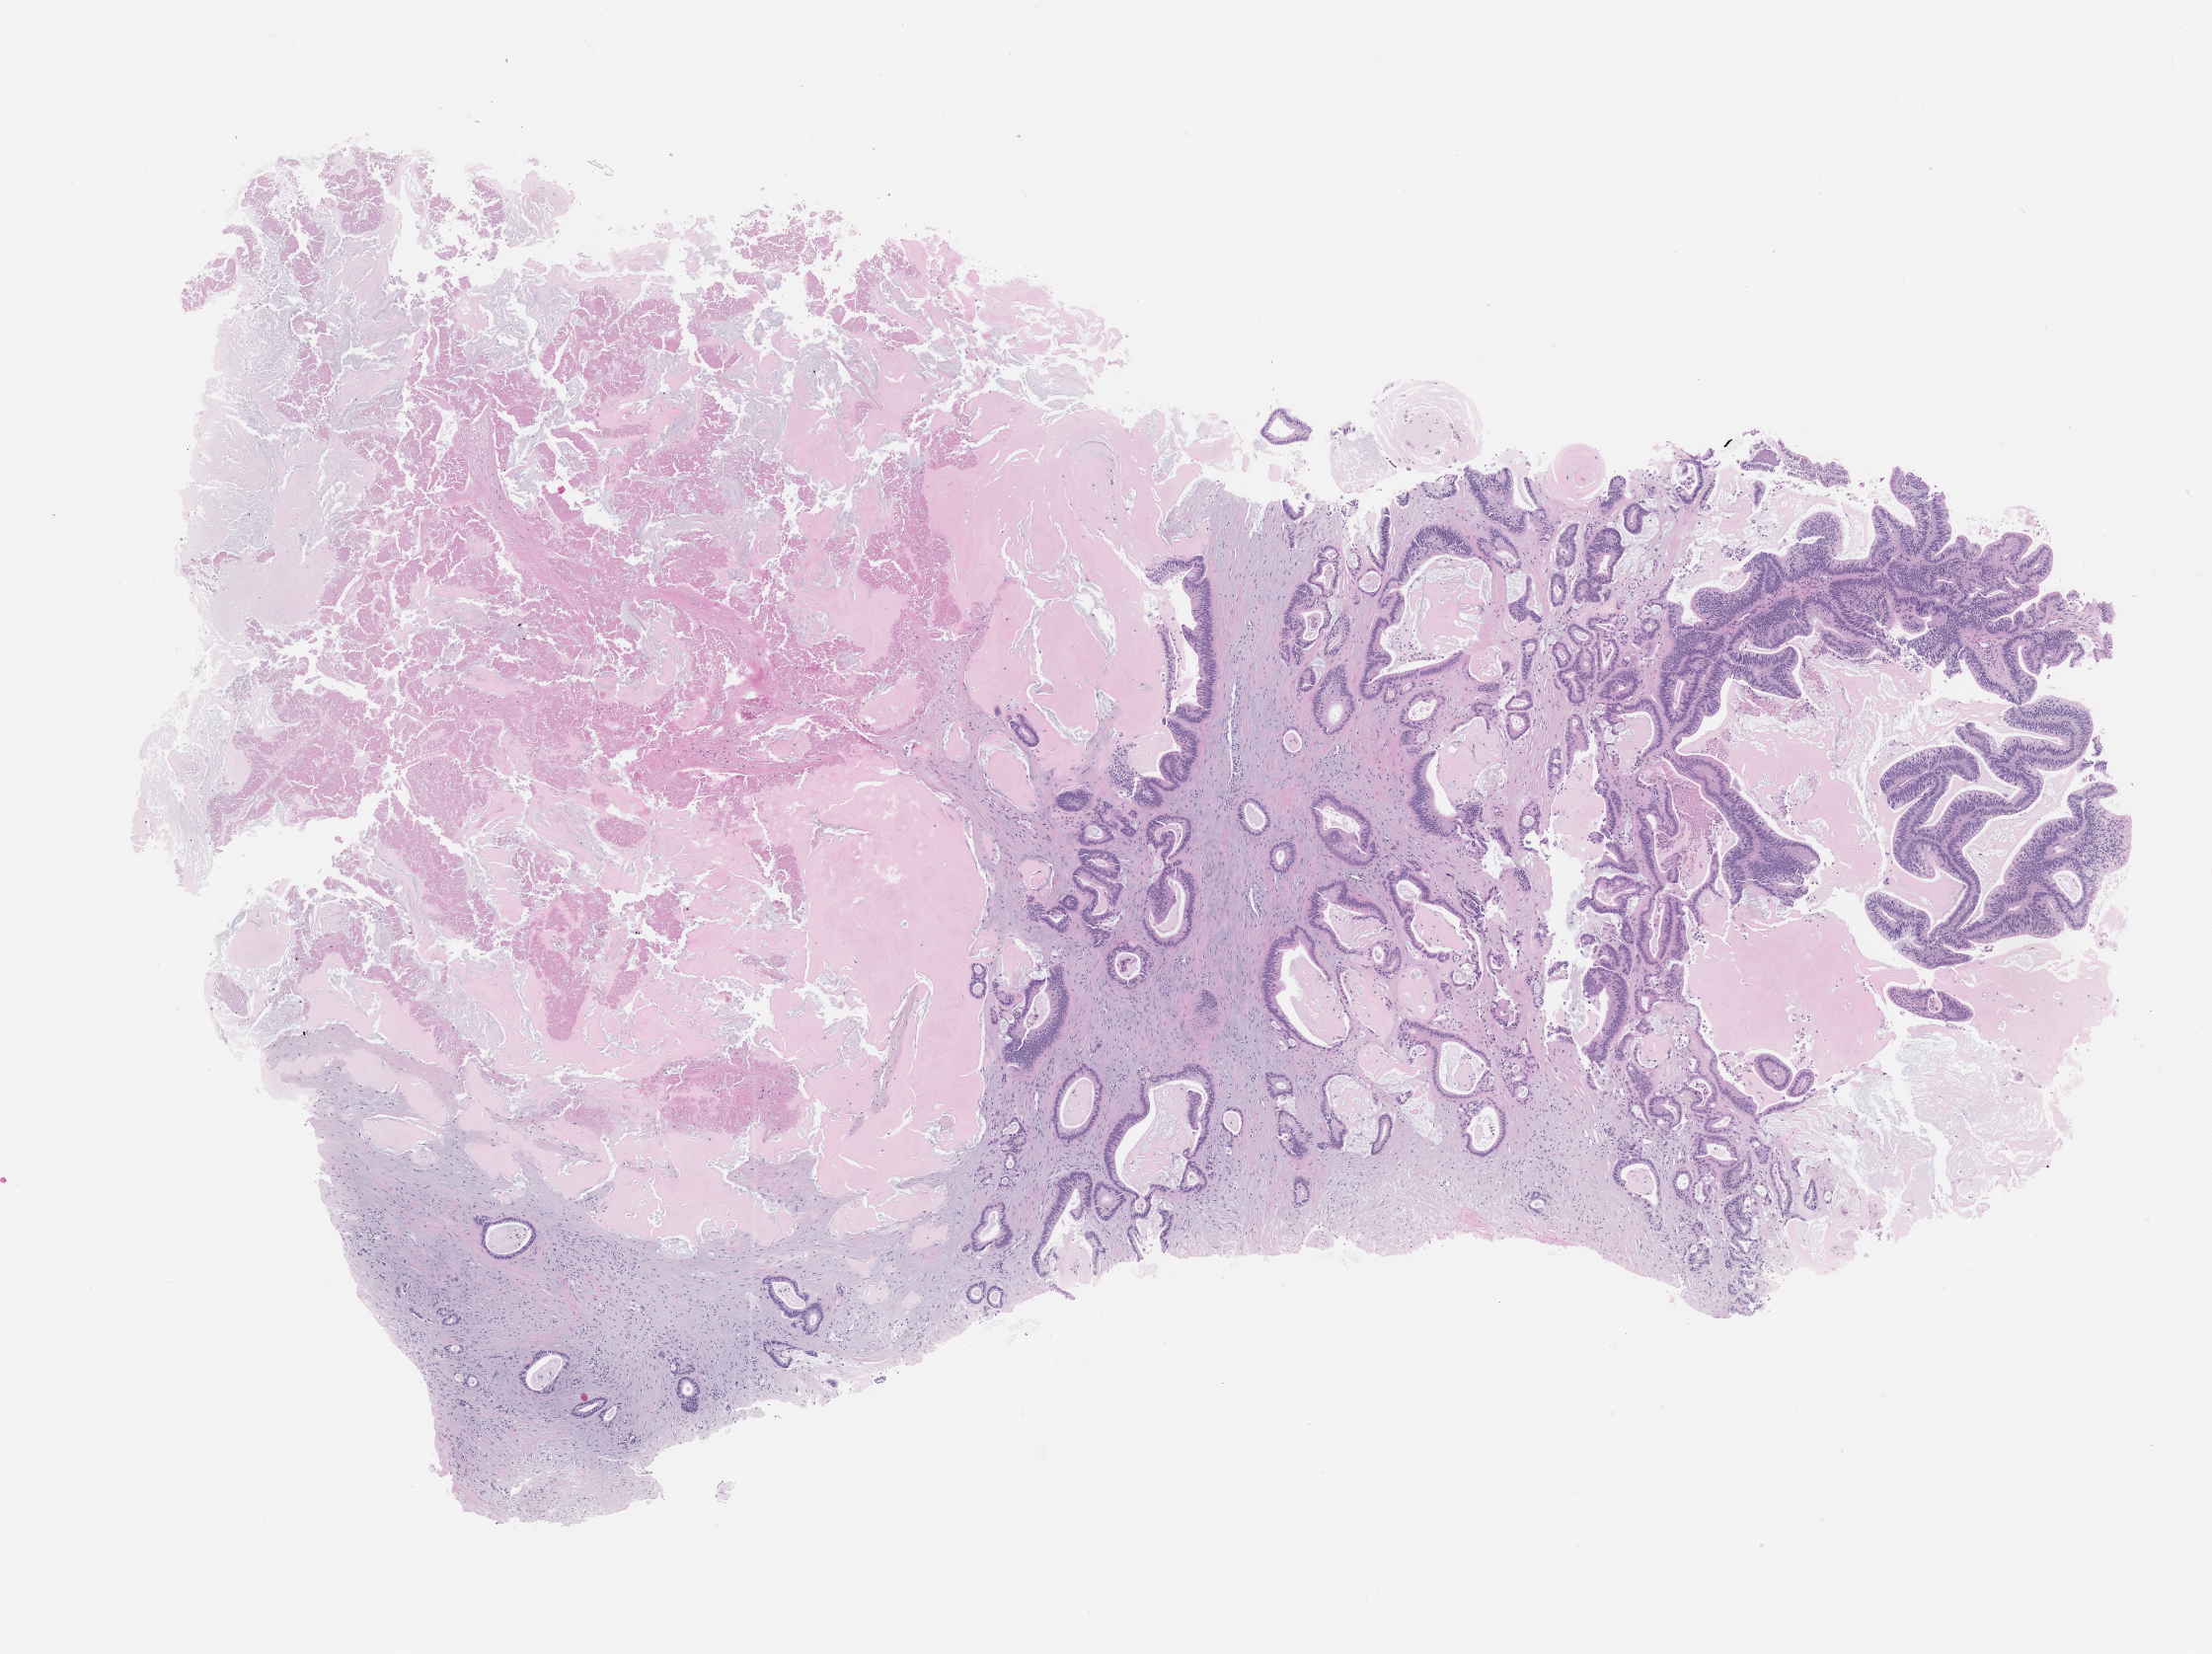
Digitized haematoxylin and eosin-stained section of the patient's (originator) tumor tissue, a low-resolution overview of the entire scanned area, about 9.0 x 6.7 mm; formalin-fixed, paraffin-embedded (FFPE) tissue; tumor site category: colon. Patient female; 43 years old.
• diagnosis: Colon Adenocarcinoma